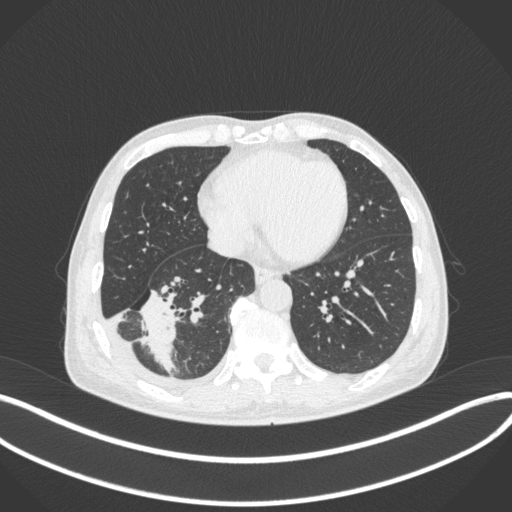
Chest CT, one axial slice; position 131 of 385 along the scan axis; reconstruction kernel B31f; lung window (W 1500 / L -600 HU); 1 mm slice thickness; 512 × 512 image matrix, field of view 400 × 400 mm. Male patient, age 64 years. Case-level facts recorded for this patient, not image findings: clinical TNM (as recorded): T3 N0 M0; histopathological grade: G2-3.
Structures marked on this image (rectangle marked by the reading radiologist):
- lung tumour (recorded histology: adenocarcinoma): bounding box [x1, y1, x2, y2] px = [137, 286, 181, 371]